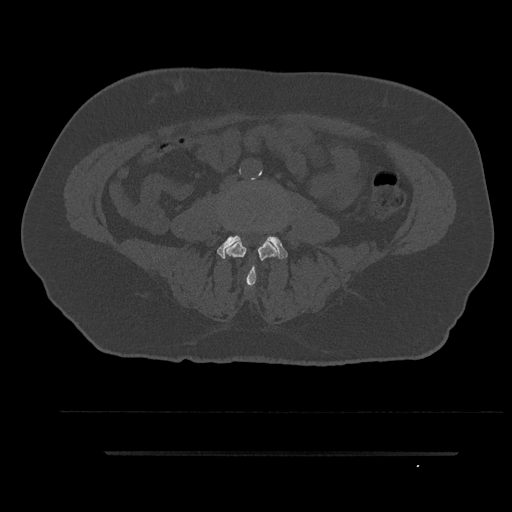
CT including the spine, one axial slice. Position 7 of 797 along the scan axis. Reconstruction kernel Br40s/3. 120 kVp. Bone window (W 1800 / L 400 HU). 512 × 512 image matrix. Patient: male, 63 years. From the clinical record (not read from this slice): primary cancer: renal.
Structures marked on this image (semi-automatically segmented with operator editing):
- L3 vertebra: bounding box (x1, y1, x2, y2) in pixels: (225, 239, 277, 285)
- L4 vertebra: (217, 235, 288, 259)